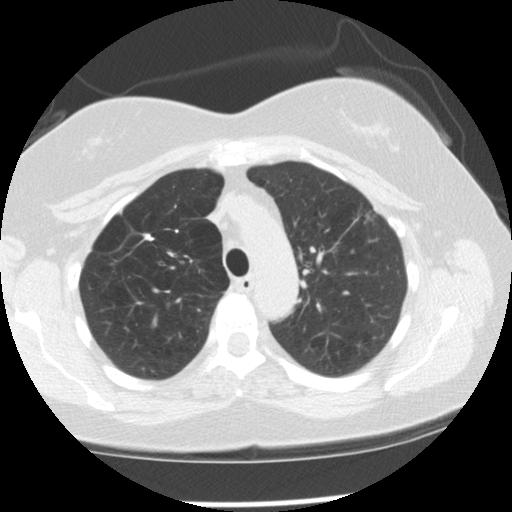
Low-dose screening chest CT, one axial slice. Position 94 of 128 along the scan axis. Reconstruction kernel STANDARD. 120 kVp. Lung window (W 1500 / L -600 HU). 2.5 mm slice thickness. 512 × 512 image matrix, field of view 319 × 319 mm.
Structures marked on this image (outlined manually by an expert reader):
- lesion 1 (tumor, upper lobe of left lung): box from (x=365, y=212) to (x=375, y=222) px